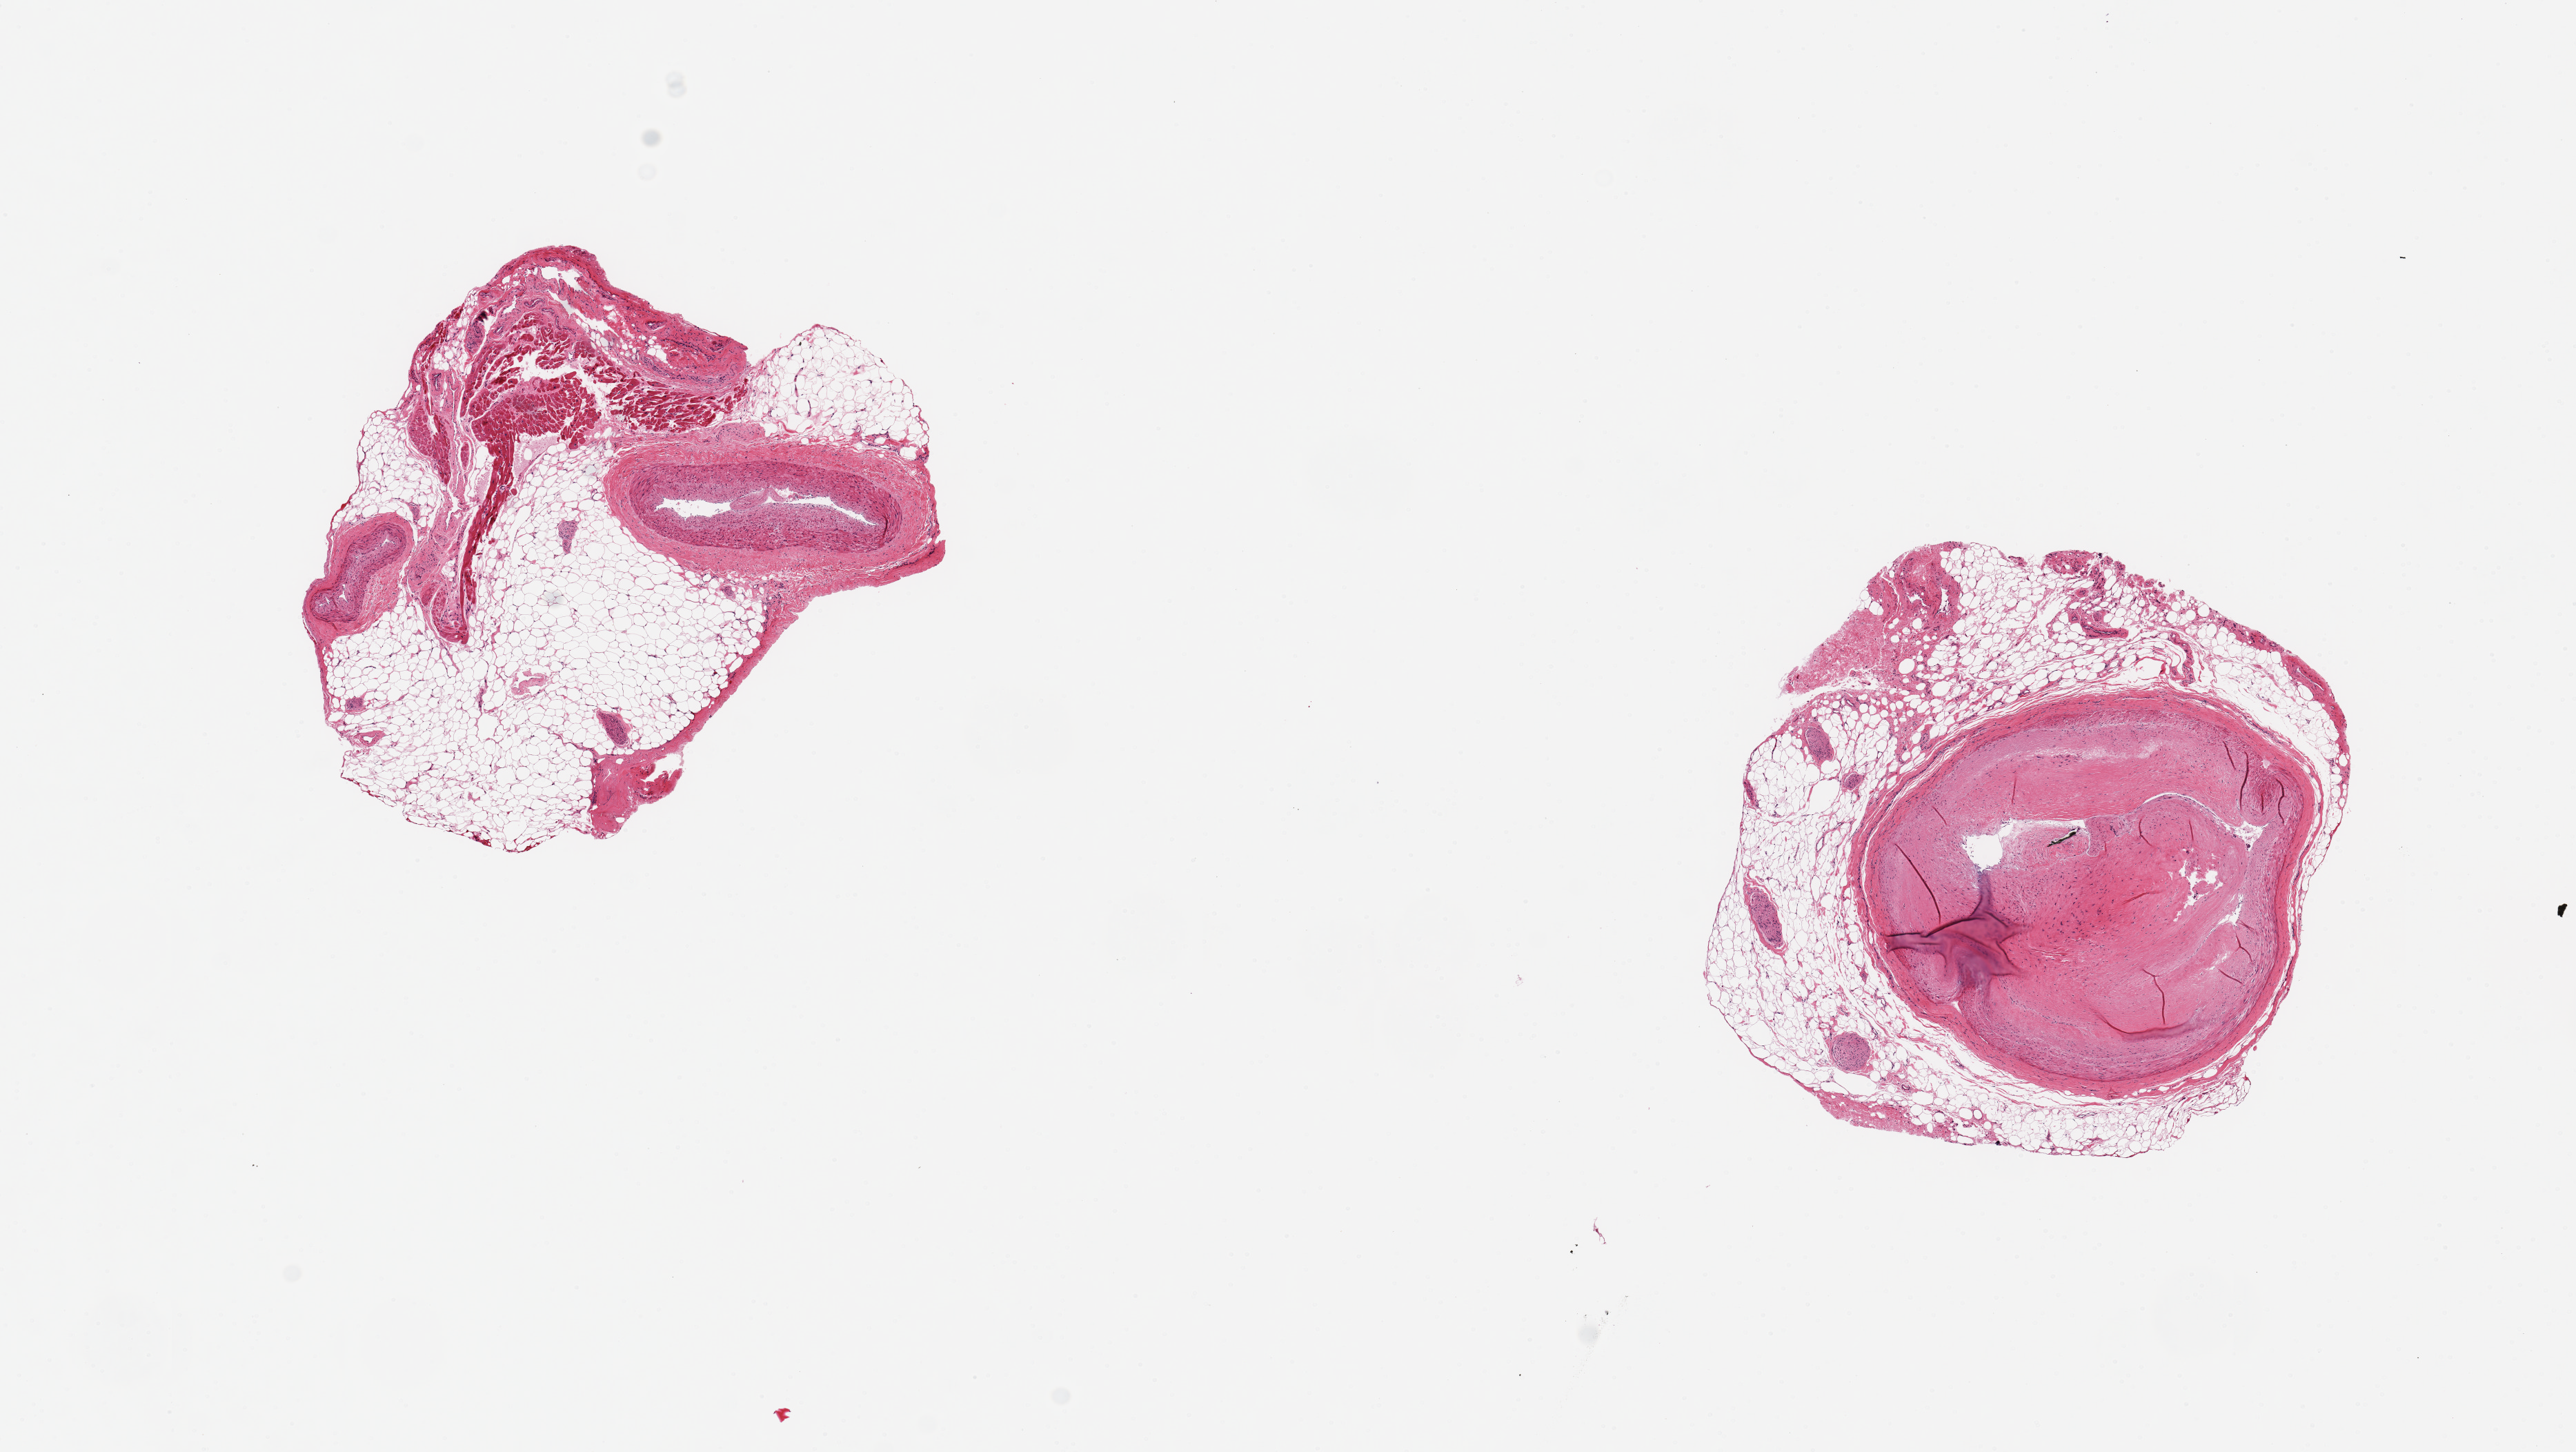
Whole-slide image, H&E stain, brightfield — a low-resolution overview of the entire scanned area, about 14.8 x 8.3 mm, PAXgene-fixed, paraffin-embedded tissue, target tissue: coronary artery, tissue donor sample. Male donor.
Review note (as recorded): 2 pieces,` 2mm d subtotally occlusive atherosclesosis. Adherent fat up to 1.5 mm in both.